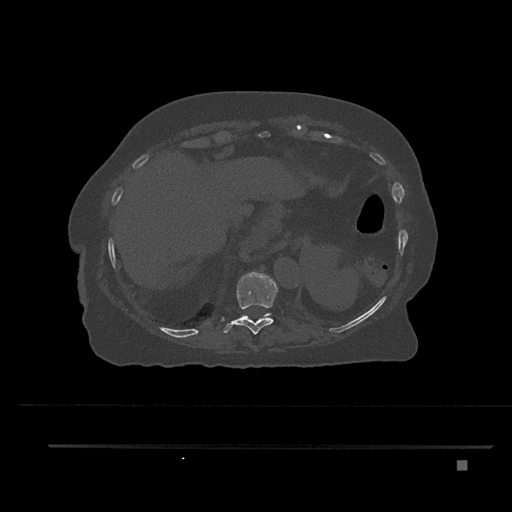
CT including the spine, one axial slice; position 350 of 797 along the scan axis; 120 kVp; bone window (W 1800 / L 400 HU); 0.5 mm slice thickness; 512 × 512 image matrix, field of view 437 × 437 mm. Patient: female, 76 years. From the clinical record (not read from this slice): primary cancer: lung; vertebrae with lytic lesions (as recorded): T11, L3.
Outlined on this slice (semi-automatically segmented with operator editing):
- T10 vertebra: bounding box (x1, y1, x2, y2) in pixels: (222, 272, 277, 335)
- T11 vertebra: (243, 313, 270, 318)